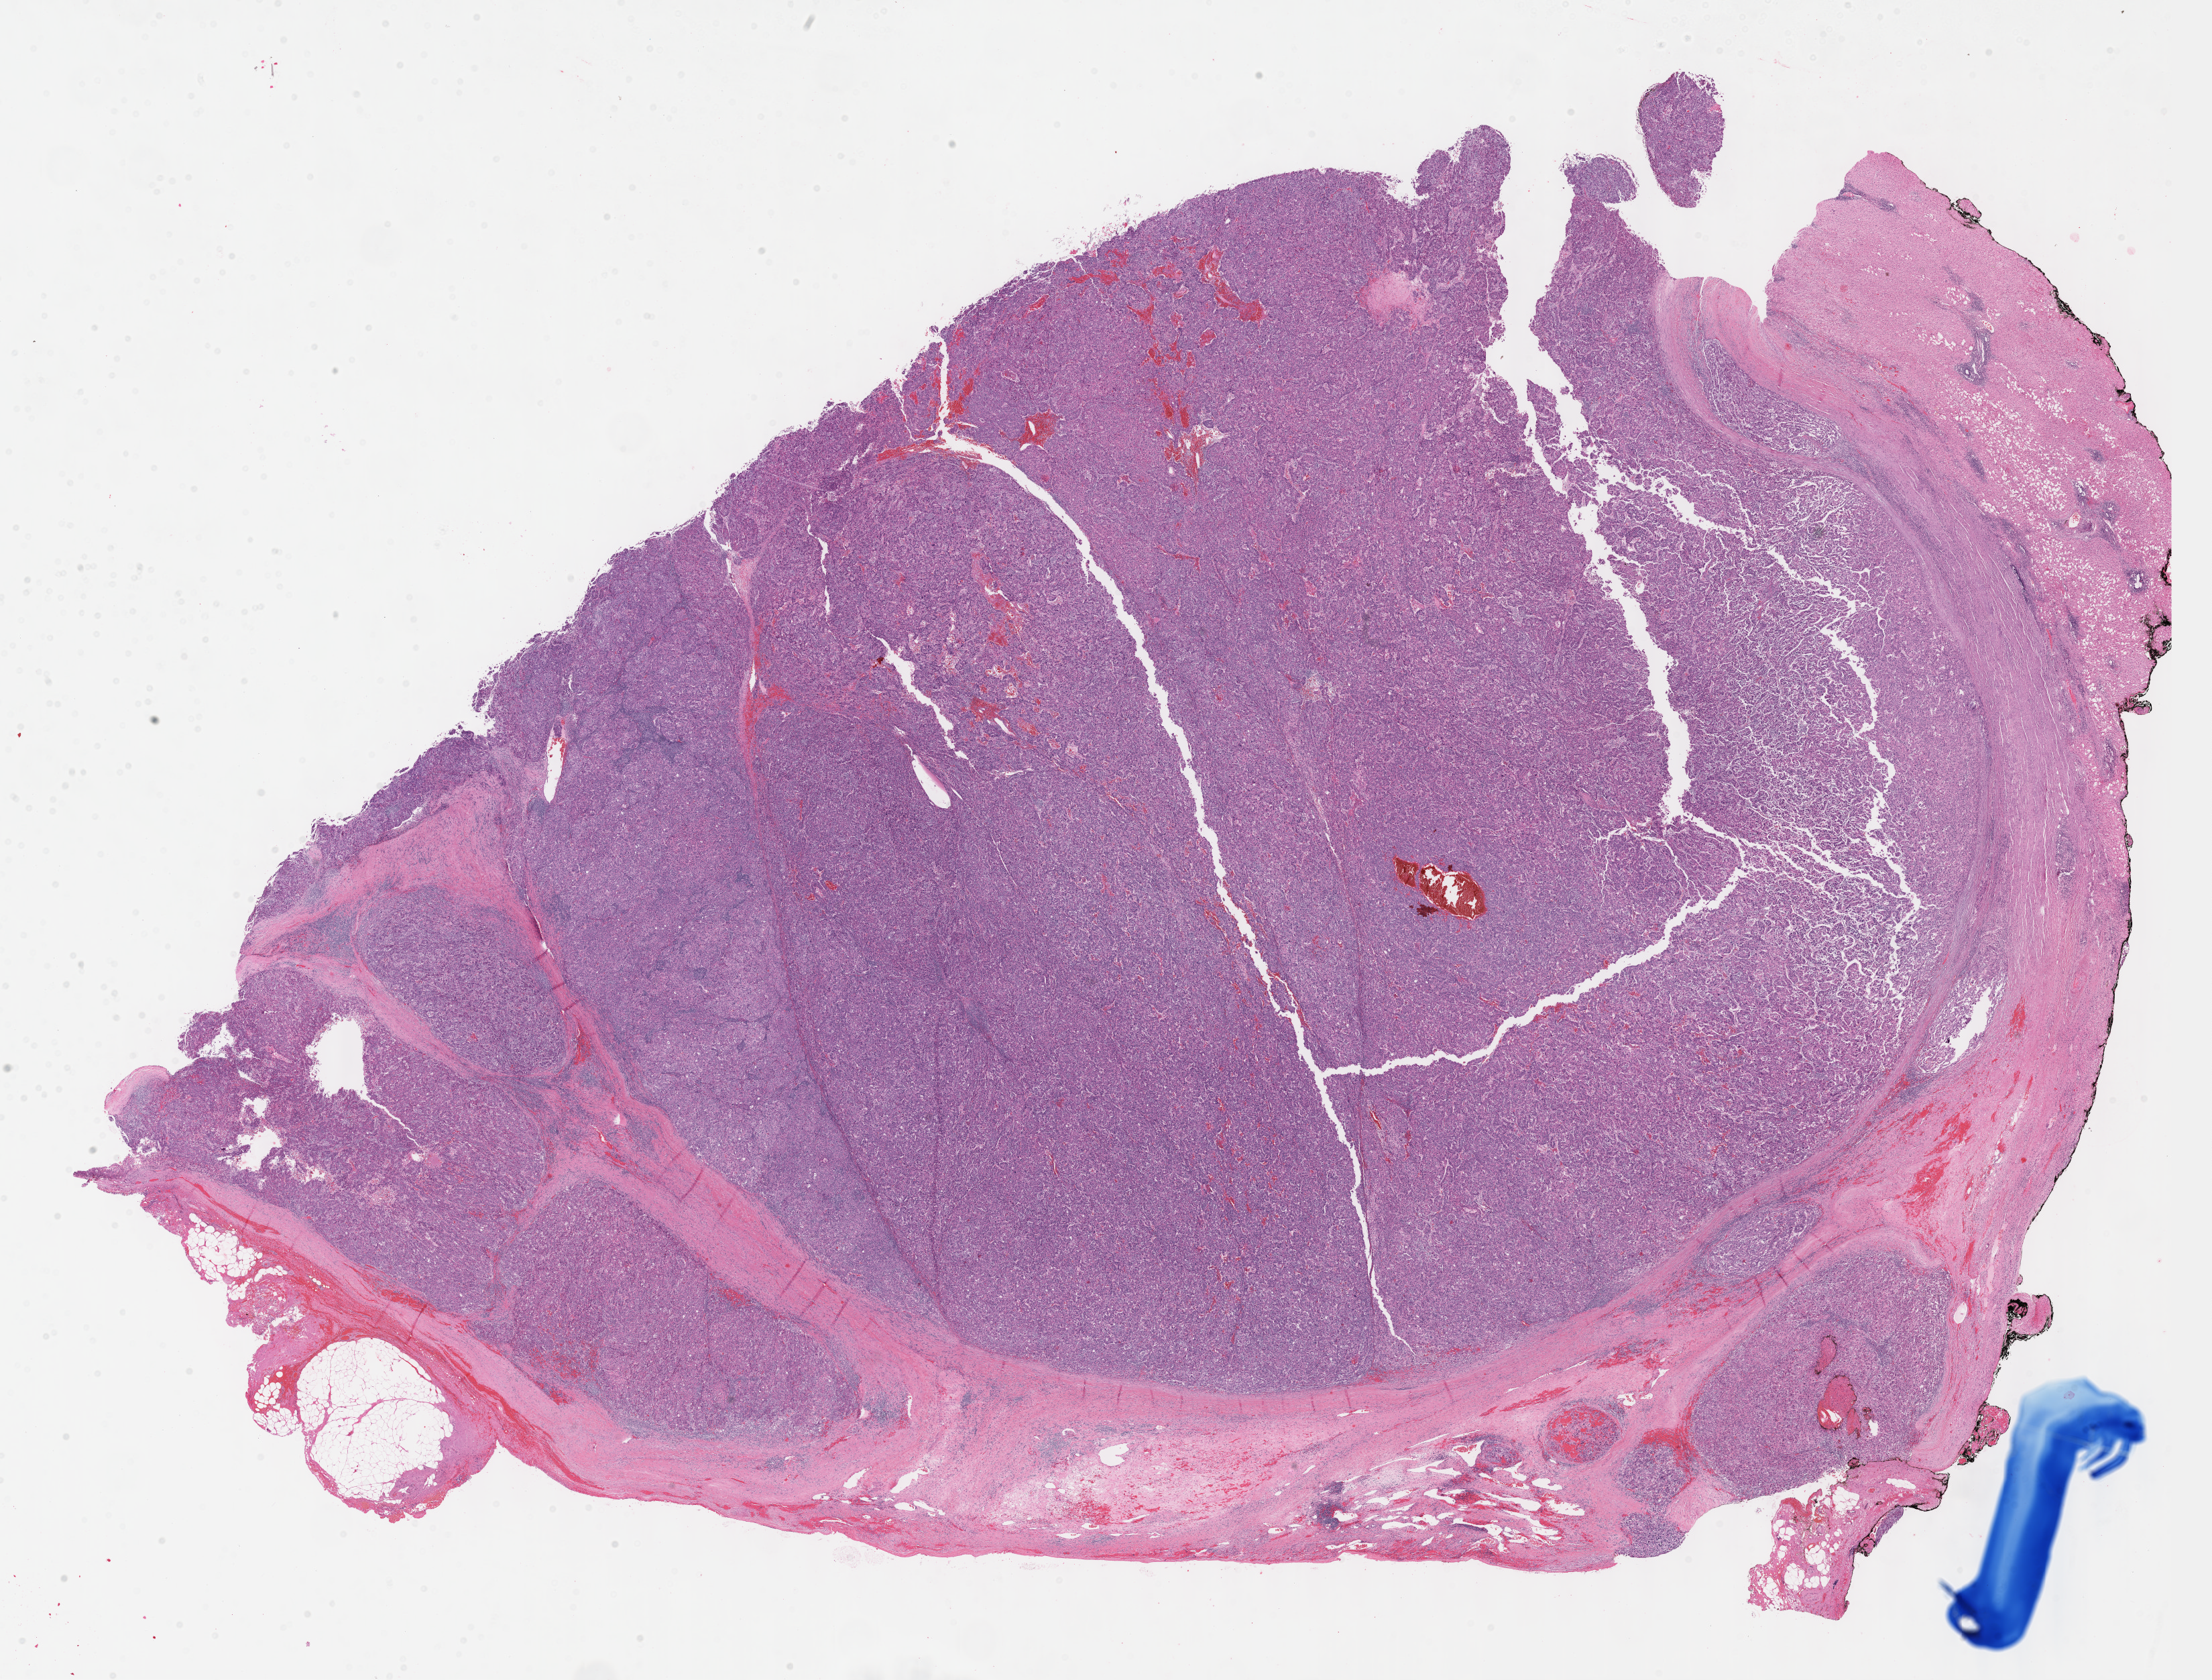
Whole-slide histology image, H&E-stained, shown as a low-resolution overview of the whole scanned area (about 26.7 x 20.2 mm, slide scanned at 40x), FFPE section, liver, primary tumour sample. Patient: male, age at initial diagnosis 69 years.
Diagnosis: Hepatocellular carcinoma, NOS.